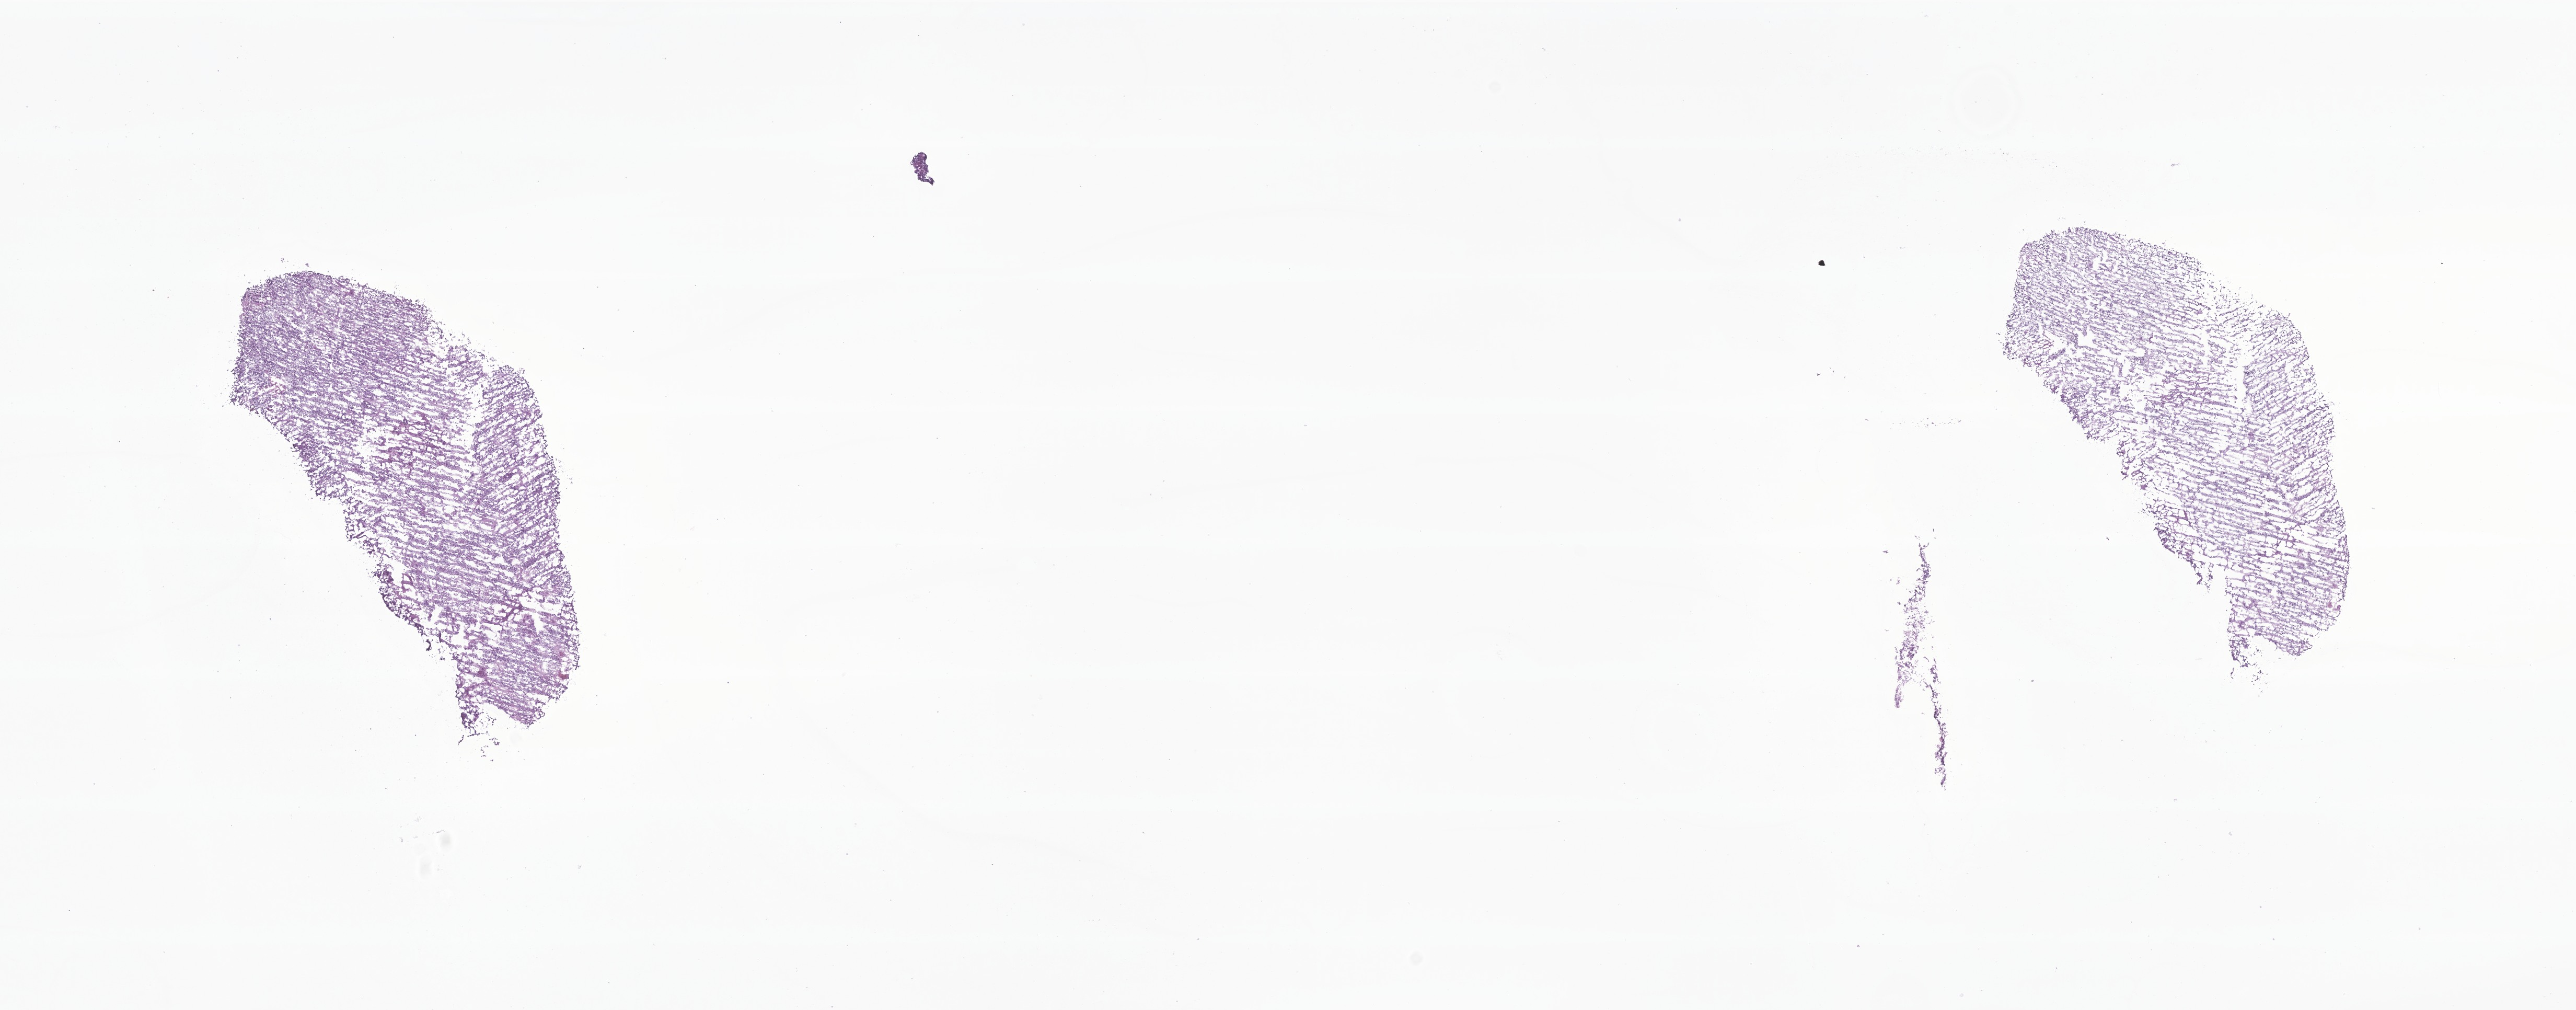
Hematoxylin and eosin (H&E) whole-slide image of tumor tissue from the brain — low-resolution overview of the scanned area, about 20.8 x 8.1 mm; frozen section (OCT-embedded). Patient: female, age 287 days.
• recorded diagnosis: Ependymoma, NOS